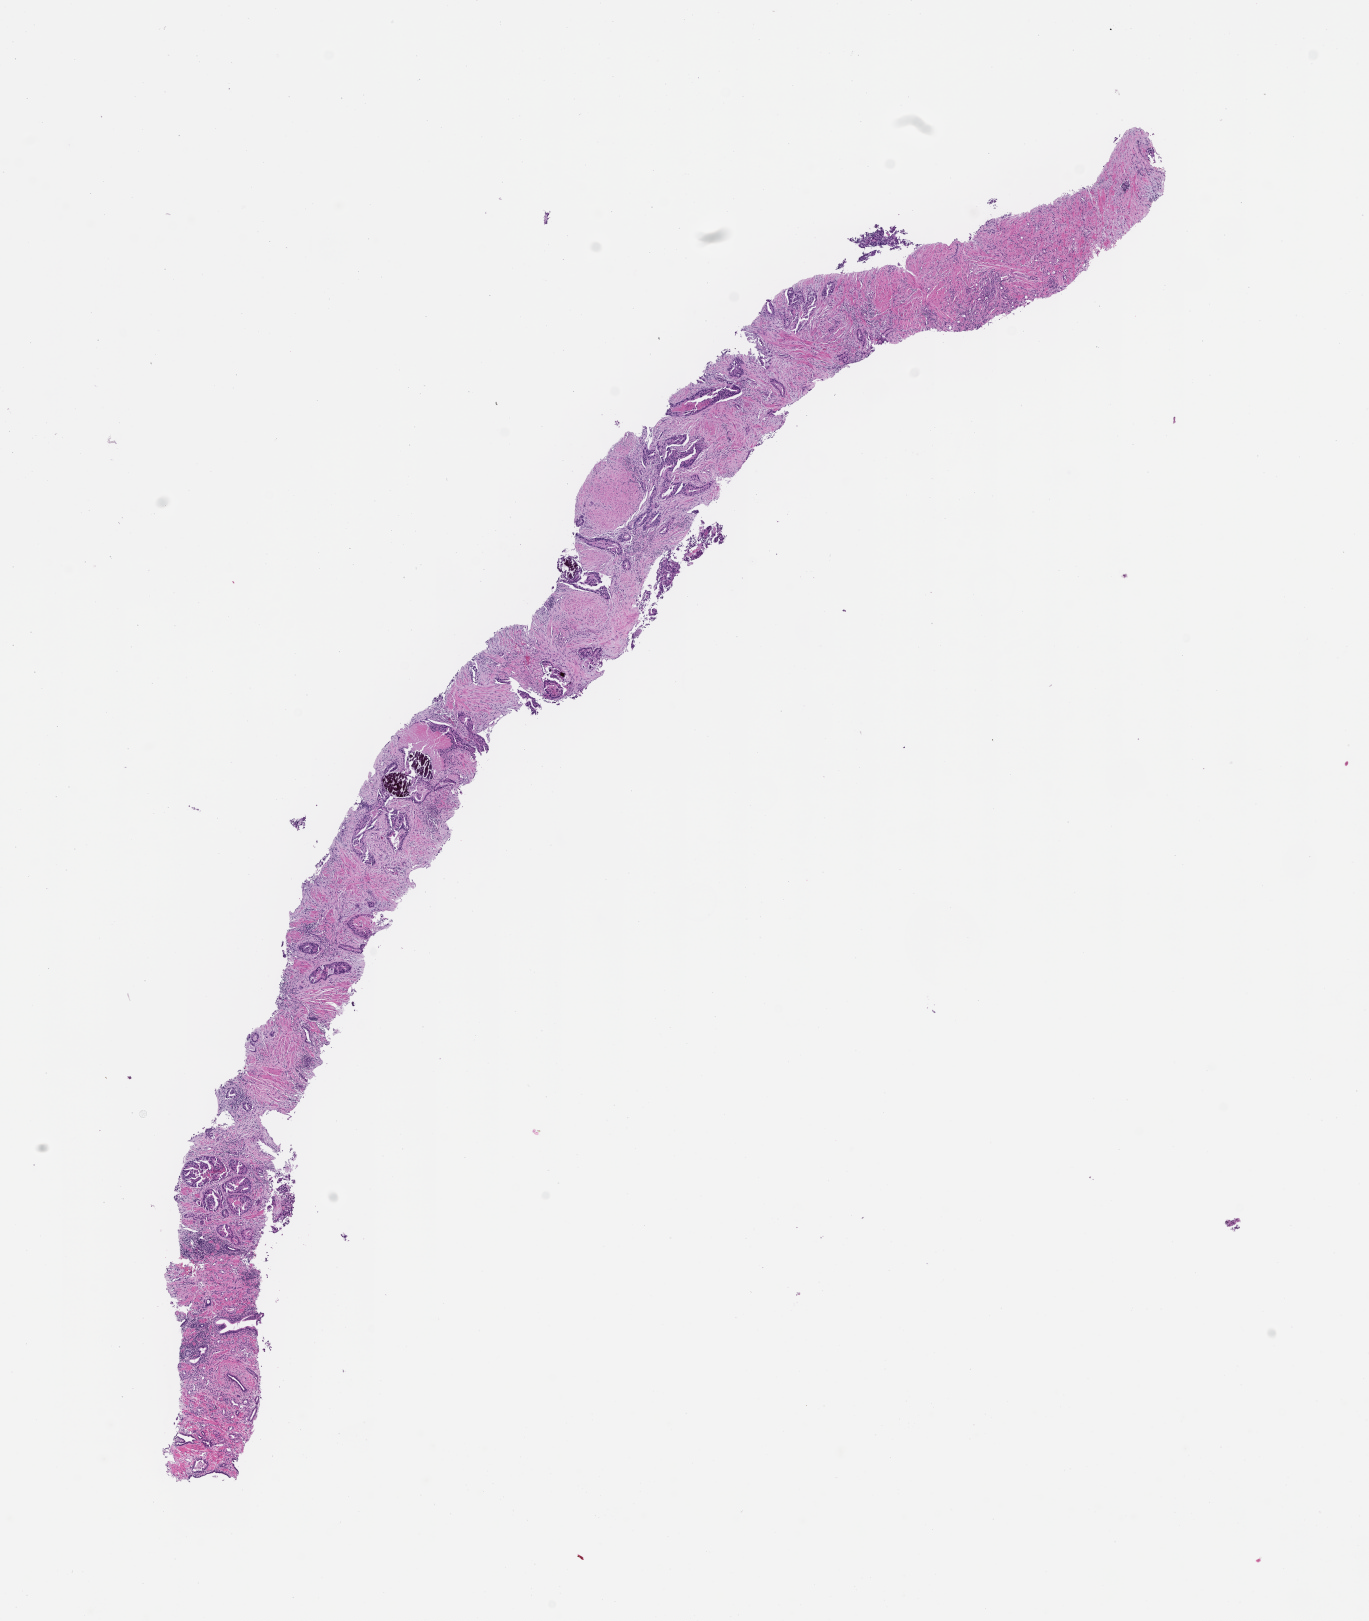
Whole-slide image, haematoxylin and eosin stain, shown as a low-resolution overview of the whole scanned area (about 11.1 x 13.1 mm); formalin-fixed, paraffin-embedded (FFPE) tissue; site: prostate. Patient: male.
This section: primary tumor. Diagnosis: Prostate Carcinoma.